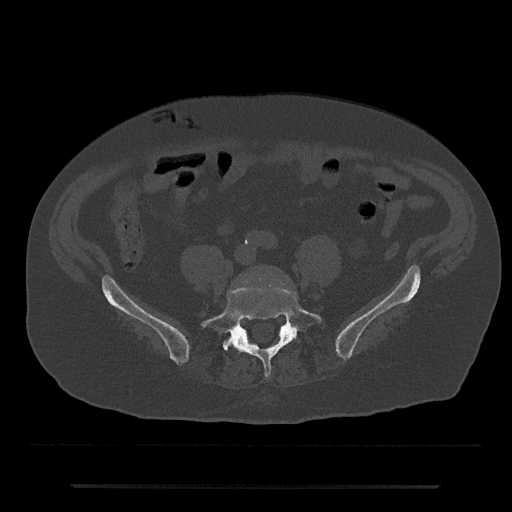
CT including the spine, one axial slice; 120 kVp; bone window (W 1800 / L 400 HU); 512 × 512 image matrix. Patient: male, 80 years. From the clinical record (not read from this slice): primary cancer: prostate; vertebrae with lytic lesions (as recorded): L1, T11.
Annotated regions visible in this slice (semi-automatically segmented with operator editing):
- L5 vertebra: bounding box [x1, y1, x2, y2] px = [201, 286, 322, 378]